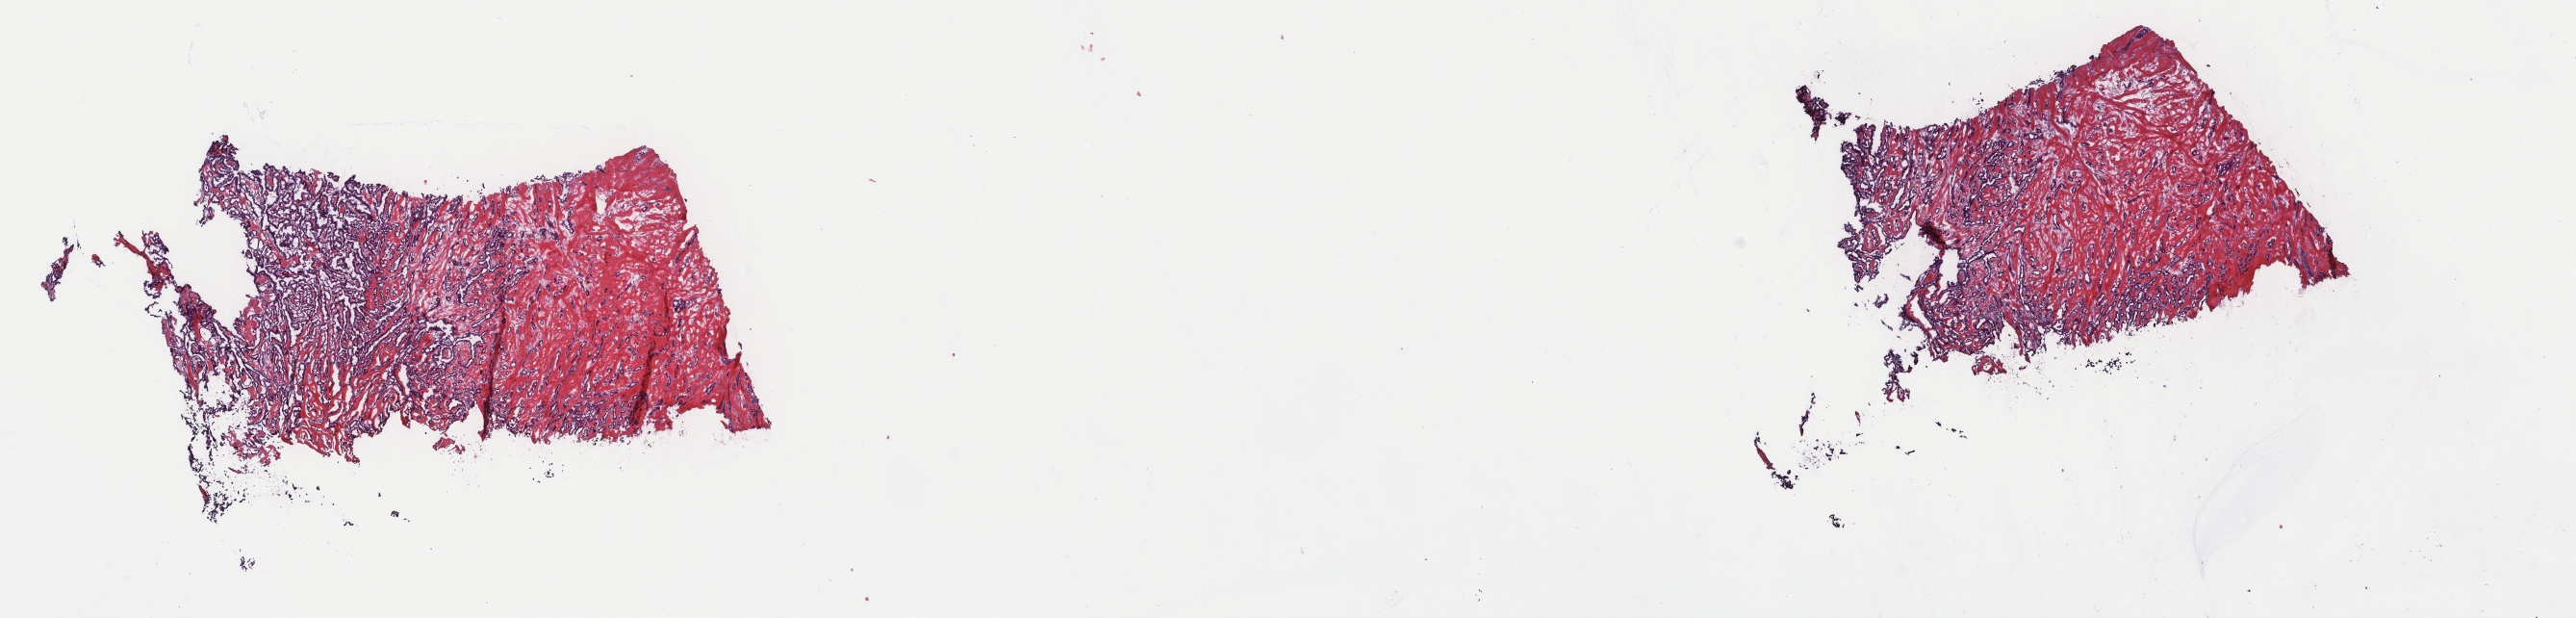
Digitized Hematoxylin and eosin (H&E) stained tissue section (whole slide) — a low-resolution overview of the entire scanned area, about 21.2 x 5.1 mm (from a 40x scan). Frozen section from the top of the tissue portion. Primary tumour sample from the thyroid. Female, age 52 years at initial diagnosis. Slide review estimates, as recorded: tumour cells 35%, tumour nuclei 100%, normal cells 0%, stromal cells 65%, necrosis 0%. Inflammatory infiltration, as recorded: lymphocyte infiltration 1%, monocyte infiltration 0%, neutrophil infiltration 0%.
Histologic diagnosis: Papillary adenocarcinoma, NOS. AJCC pathologic stage: III (7th edition). Lymph nodes positive (case pathology): 7 of 11 examined. Laterality: left.